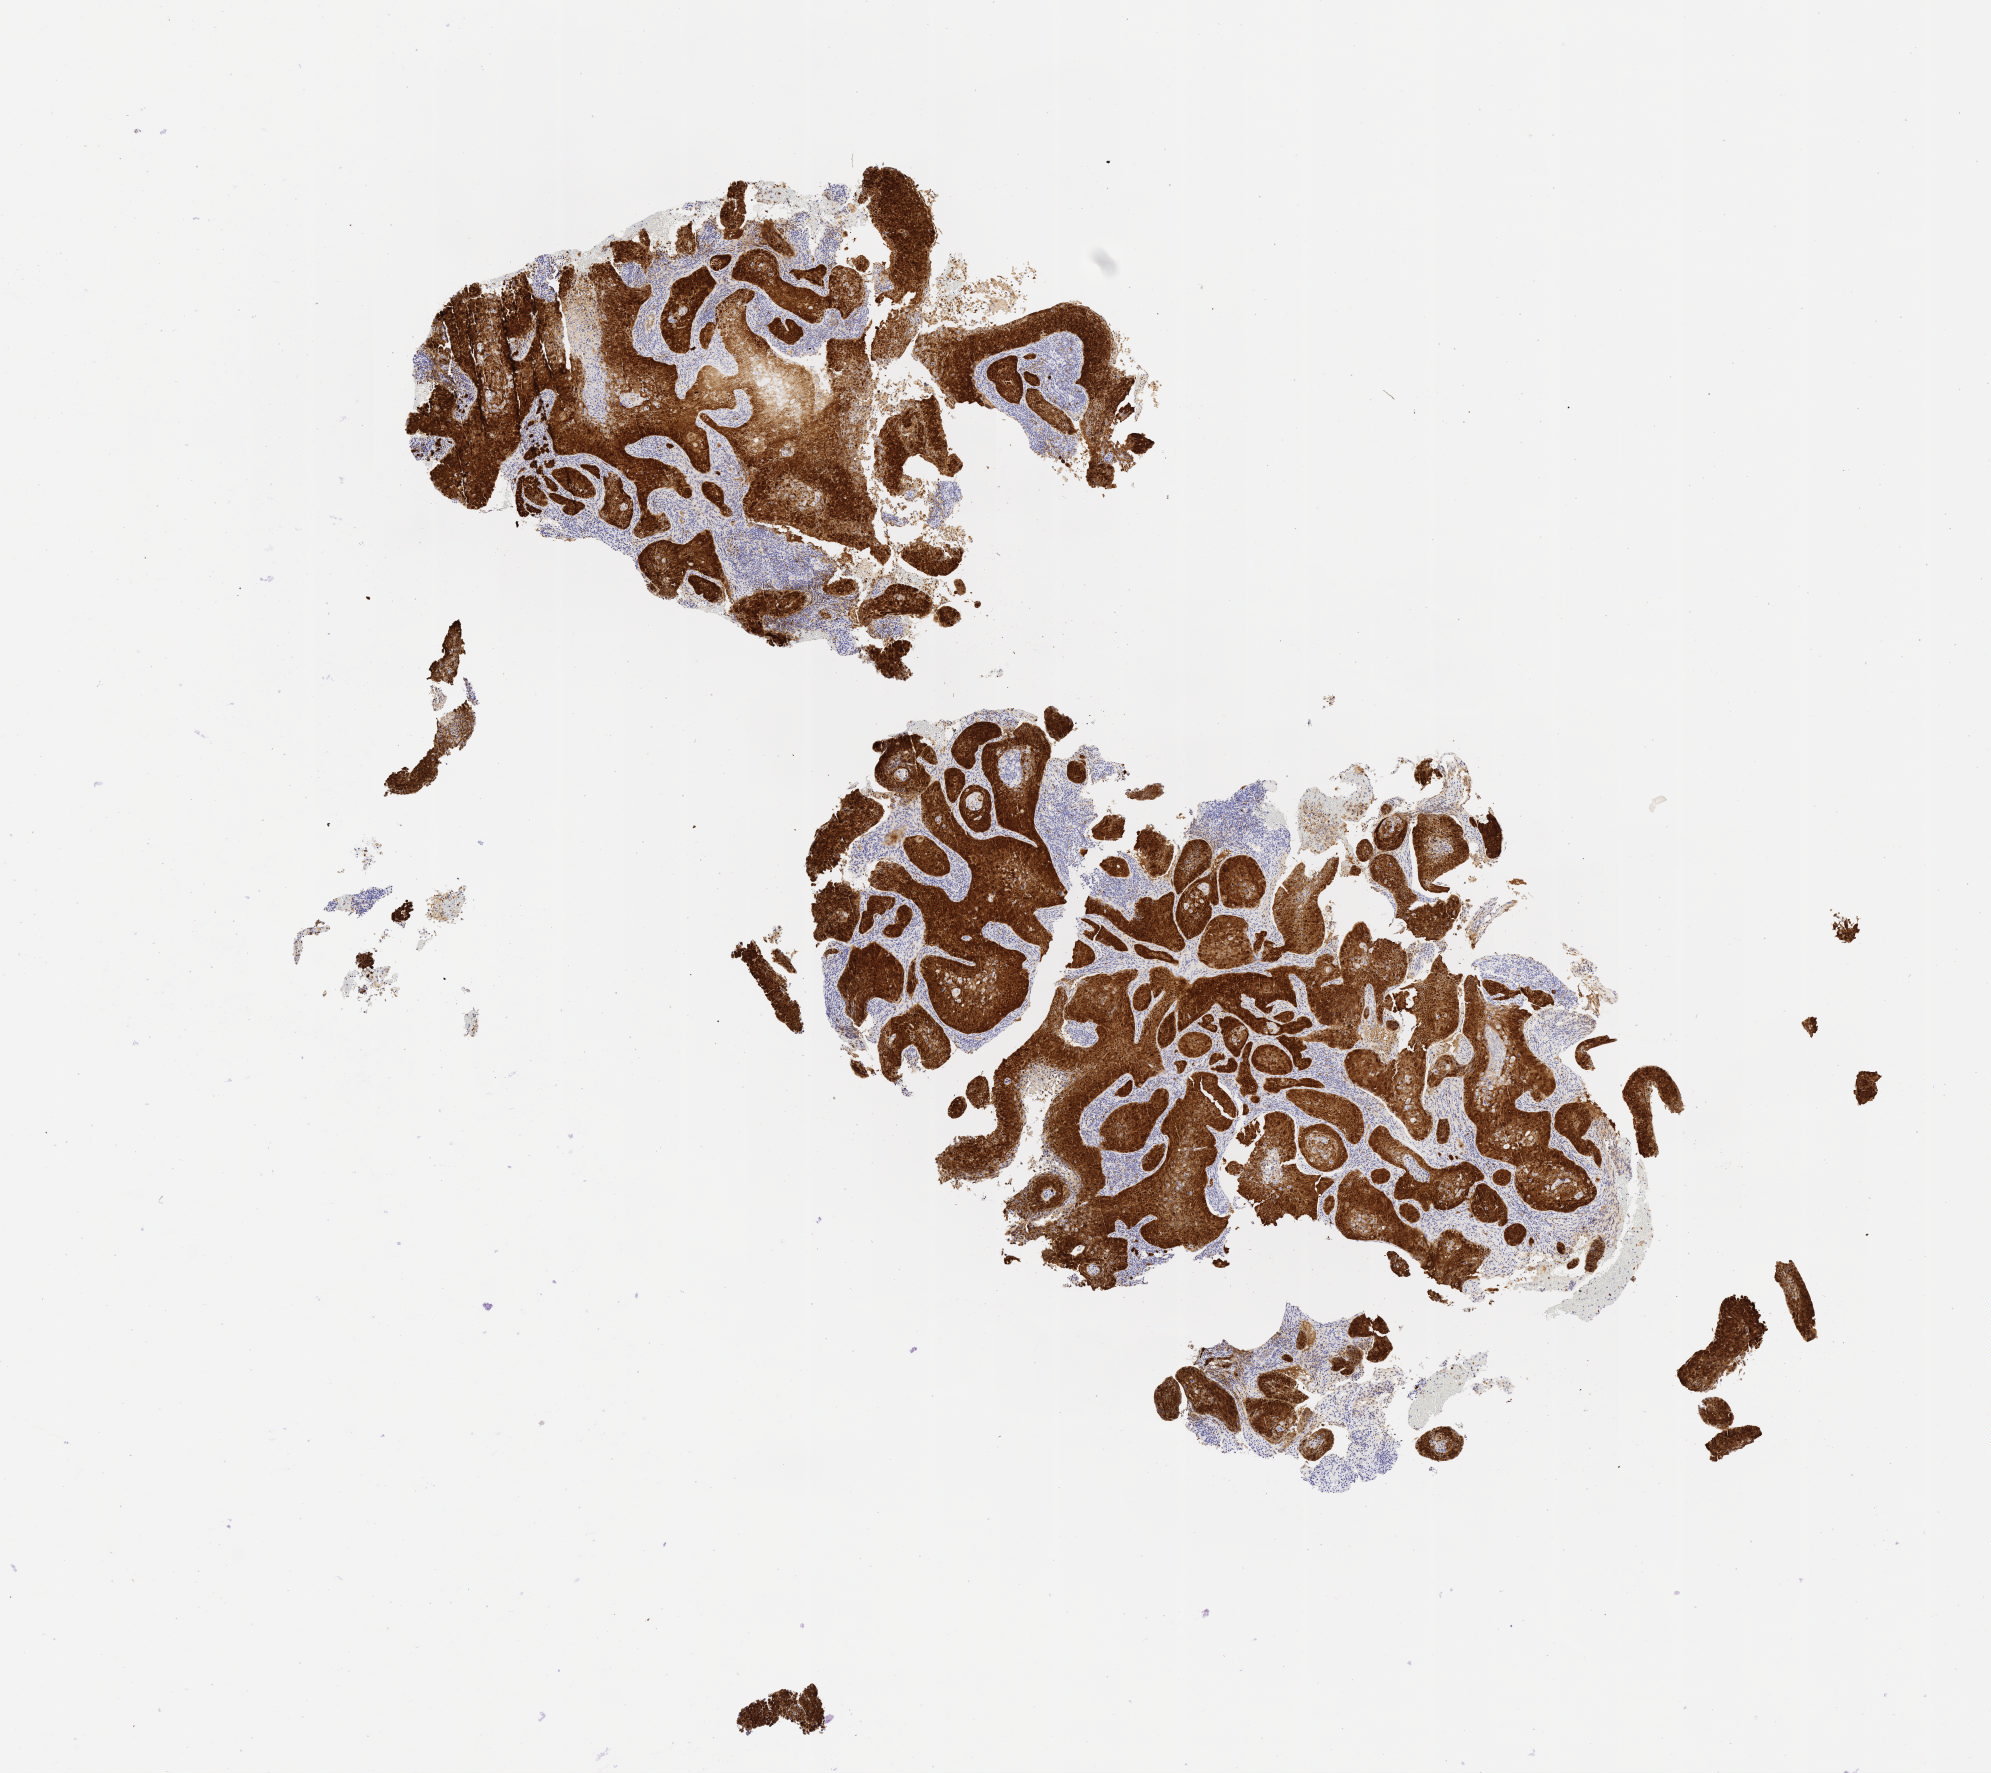
IHC for p16 (p16INK4a), whole-slide image — low-resolution overview of the scanned area, about 8.1 x 7.2 mm; tumor tissue; anatomic site: cervix. Patient: female, aged 41.
Histologic diagnosis: Squamous cell carcinoma, large cell, nonkeratinizing, NOS.